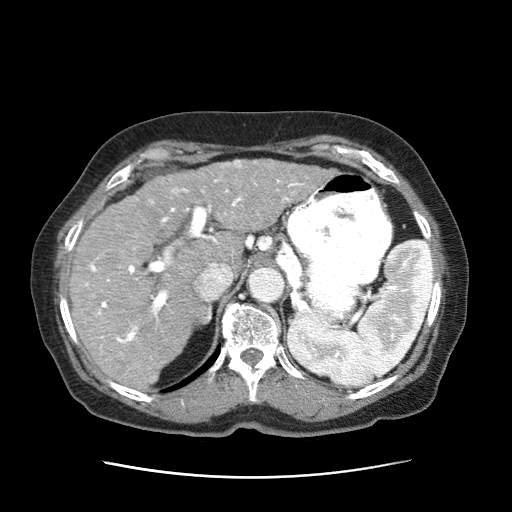
Contrast-enhanced abdominal CT (liver protocol), one axial slice; position 44 of 63 along the scan axis; reconstruction kernel STANDARD; intravenous contrast given; soft-tissue window (W 400 / L 40 HU); 512 × 512 image matrix. Female patient, age 79 years. From the clinical record (not read from this slice): diagnosis: hepatocellular carcinoma (patient treated with transarterial chemoembolisation; whether this scan precedes or follows treatment is not stated here); TNM stage (as recorded): Stage-II; Child-Pugh class: B; tumour nodularity: multinodular; tumour size: 5 cm.
Structures marked on this image (semi-automatic segmentation, software-assisted and operator-edited):
- abdominal aorta: bounding box [x1, y1, x2, y2] px = [247, 267, 284, 302]
- liver parenchyma outside the tumour (the mass and vessels are separate outlines, so this box may not span the whole liver): [70, 171, 245, 391]
- mass: [187, 160, 331, 232]
- liver vessels: [85, 179, 304, 344]